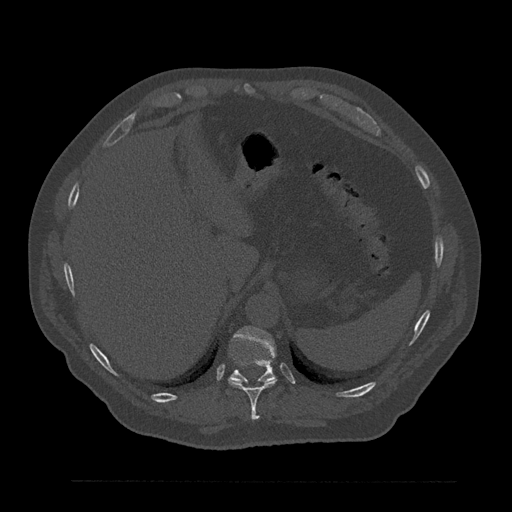
CT including the spine, one axial slice; slice 325 of 797 in the series (ordered by position); 120 kVp; bone window (W 1800 / L 400 HU); 0.5 mm slice thickness; 512 × 512 image matrix, field of view 430 × 430 mm. Male patient, age 61 years. From the clinical record (not read from this slice): primary cancer: prostate.
Annotated regions visible in this slice (semi-automatic segmentation, software-assisted and operator-edited):
- T10 vertebra: bounding box [x1, y1, x2, y2] px = [228, 378, 277, 420]
- T11 vertebra: [230, 326, 276, 383]